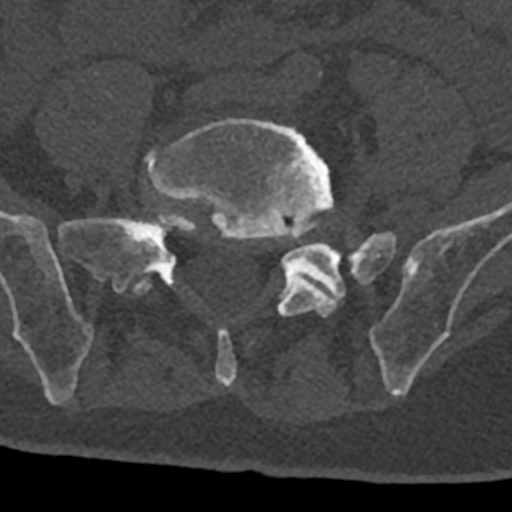
CT including the spine, one axial slice; position 178 of 797 along the scan axis; bone window (W 1800 / L 400 HU); 0.5 mm slice thickness; 512 × 512 image matrix, field of view 160 × 160 mm. Male patient, age 74 years. Case-level facts recorded for this patient, not image findings: primary cancer: renal; vertebrae with lytic lesions (as recorded): T10, L1, L2, L3, L4, L5.
Annotated regions visible in this slice (semi-automatic segmentation, software-assisted and operator-edited):
- L5 vertebra: box from (x=134, y=118) to (x=353, y=386) px